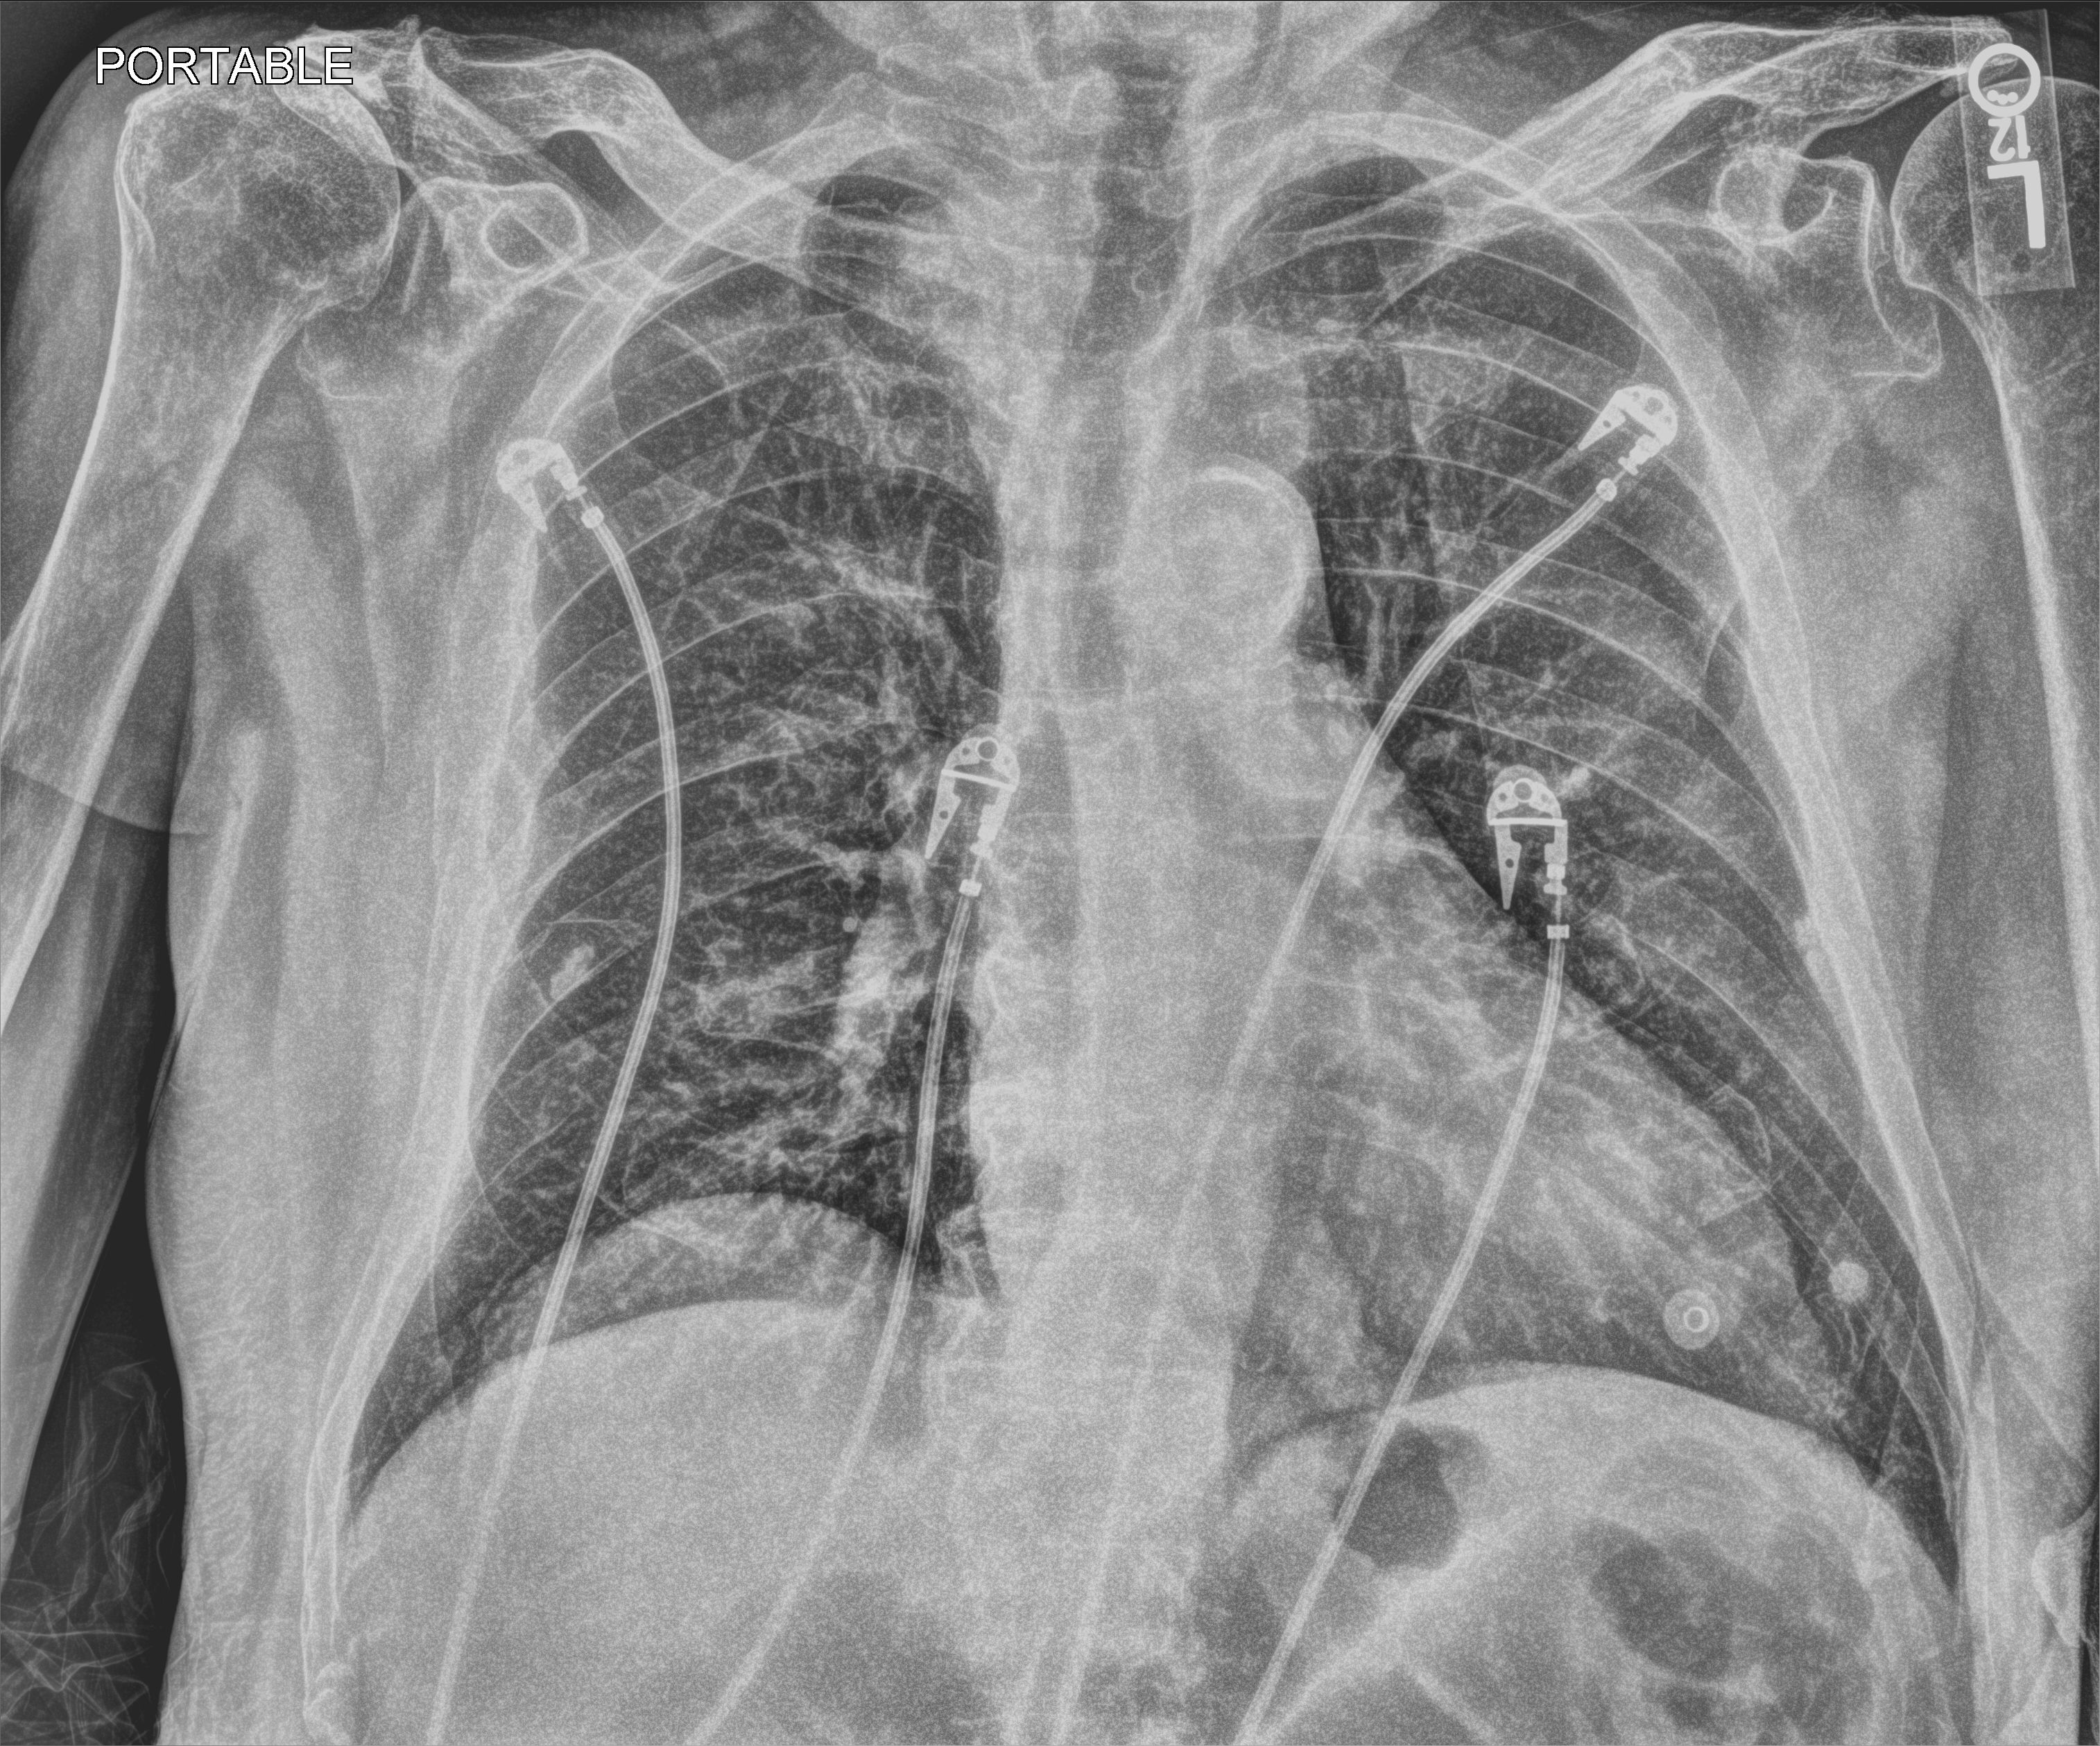
Bedside chest radiograph (computed radiography). Male patient hospitalised with COVID-19, age 75–90 years.
Admission-level facts for this patient (not findings on this image; timing relative to this image not recorded): admitted to intensive care during this hospital stay: no.